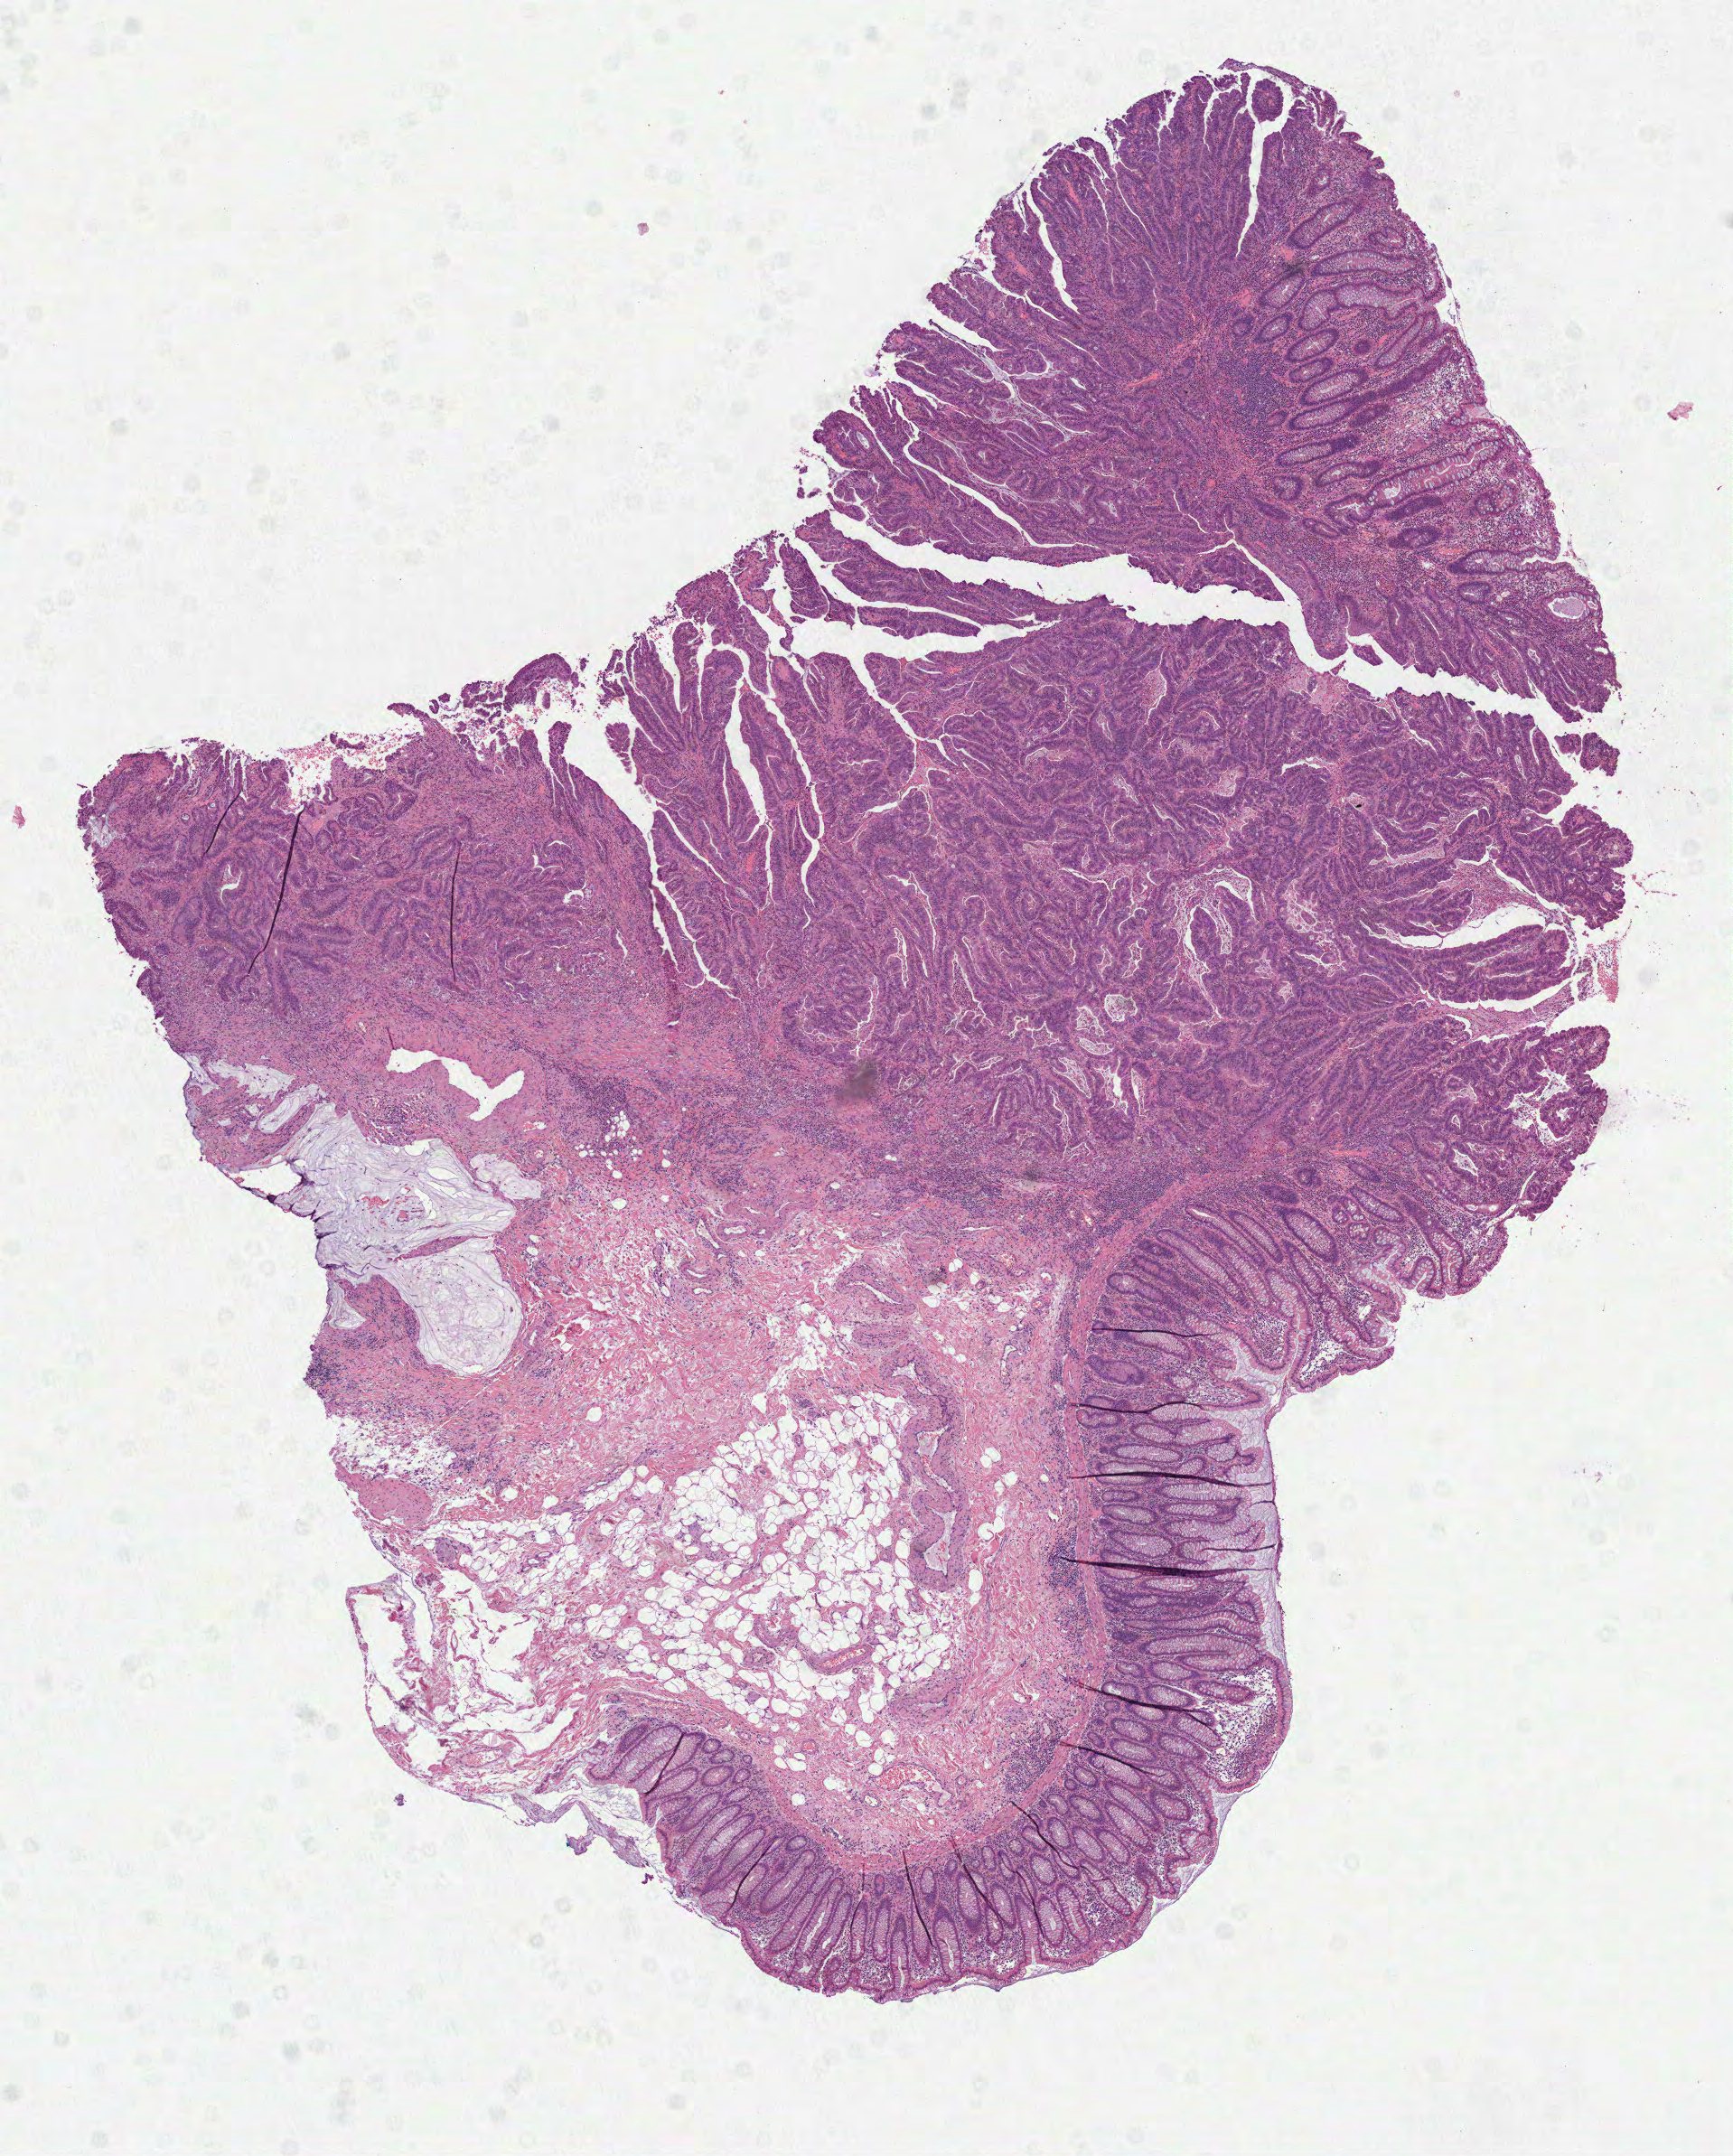
H&E-stained whole-slide image, shown as a low-resolution overview of the whole scanned area (about 7.7 x 9.6 mm, from a 40x scan); formalin-fixed paraffin-embedded (FFPE) diagnostic section; primary tumour sample from the colon. Male, age 67 years at initial diagnosis.
AJCC pathologic stage: I (7th edition). Pathologic diagnosis: Mucinous adenocarcinoma (ascending colon). Lymph nodes positive (case pathology): 0 of 11 examined.